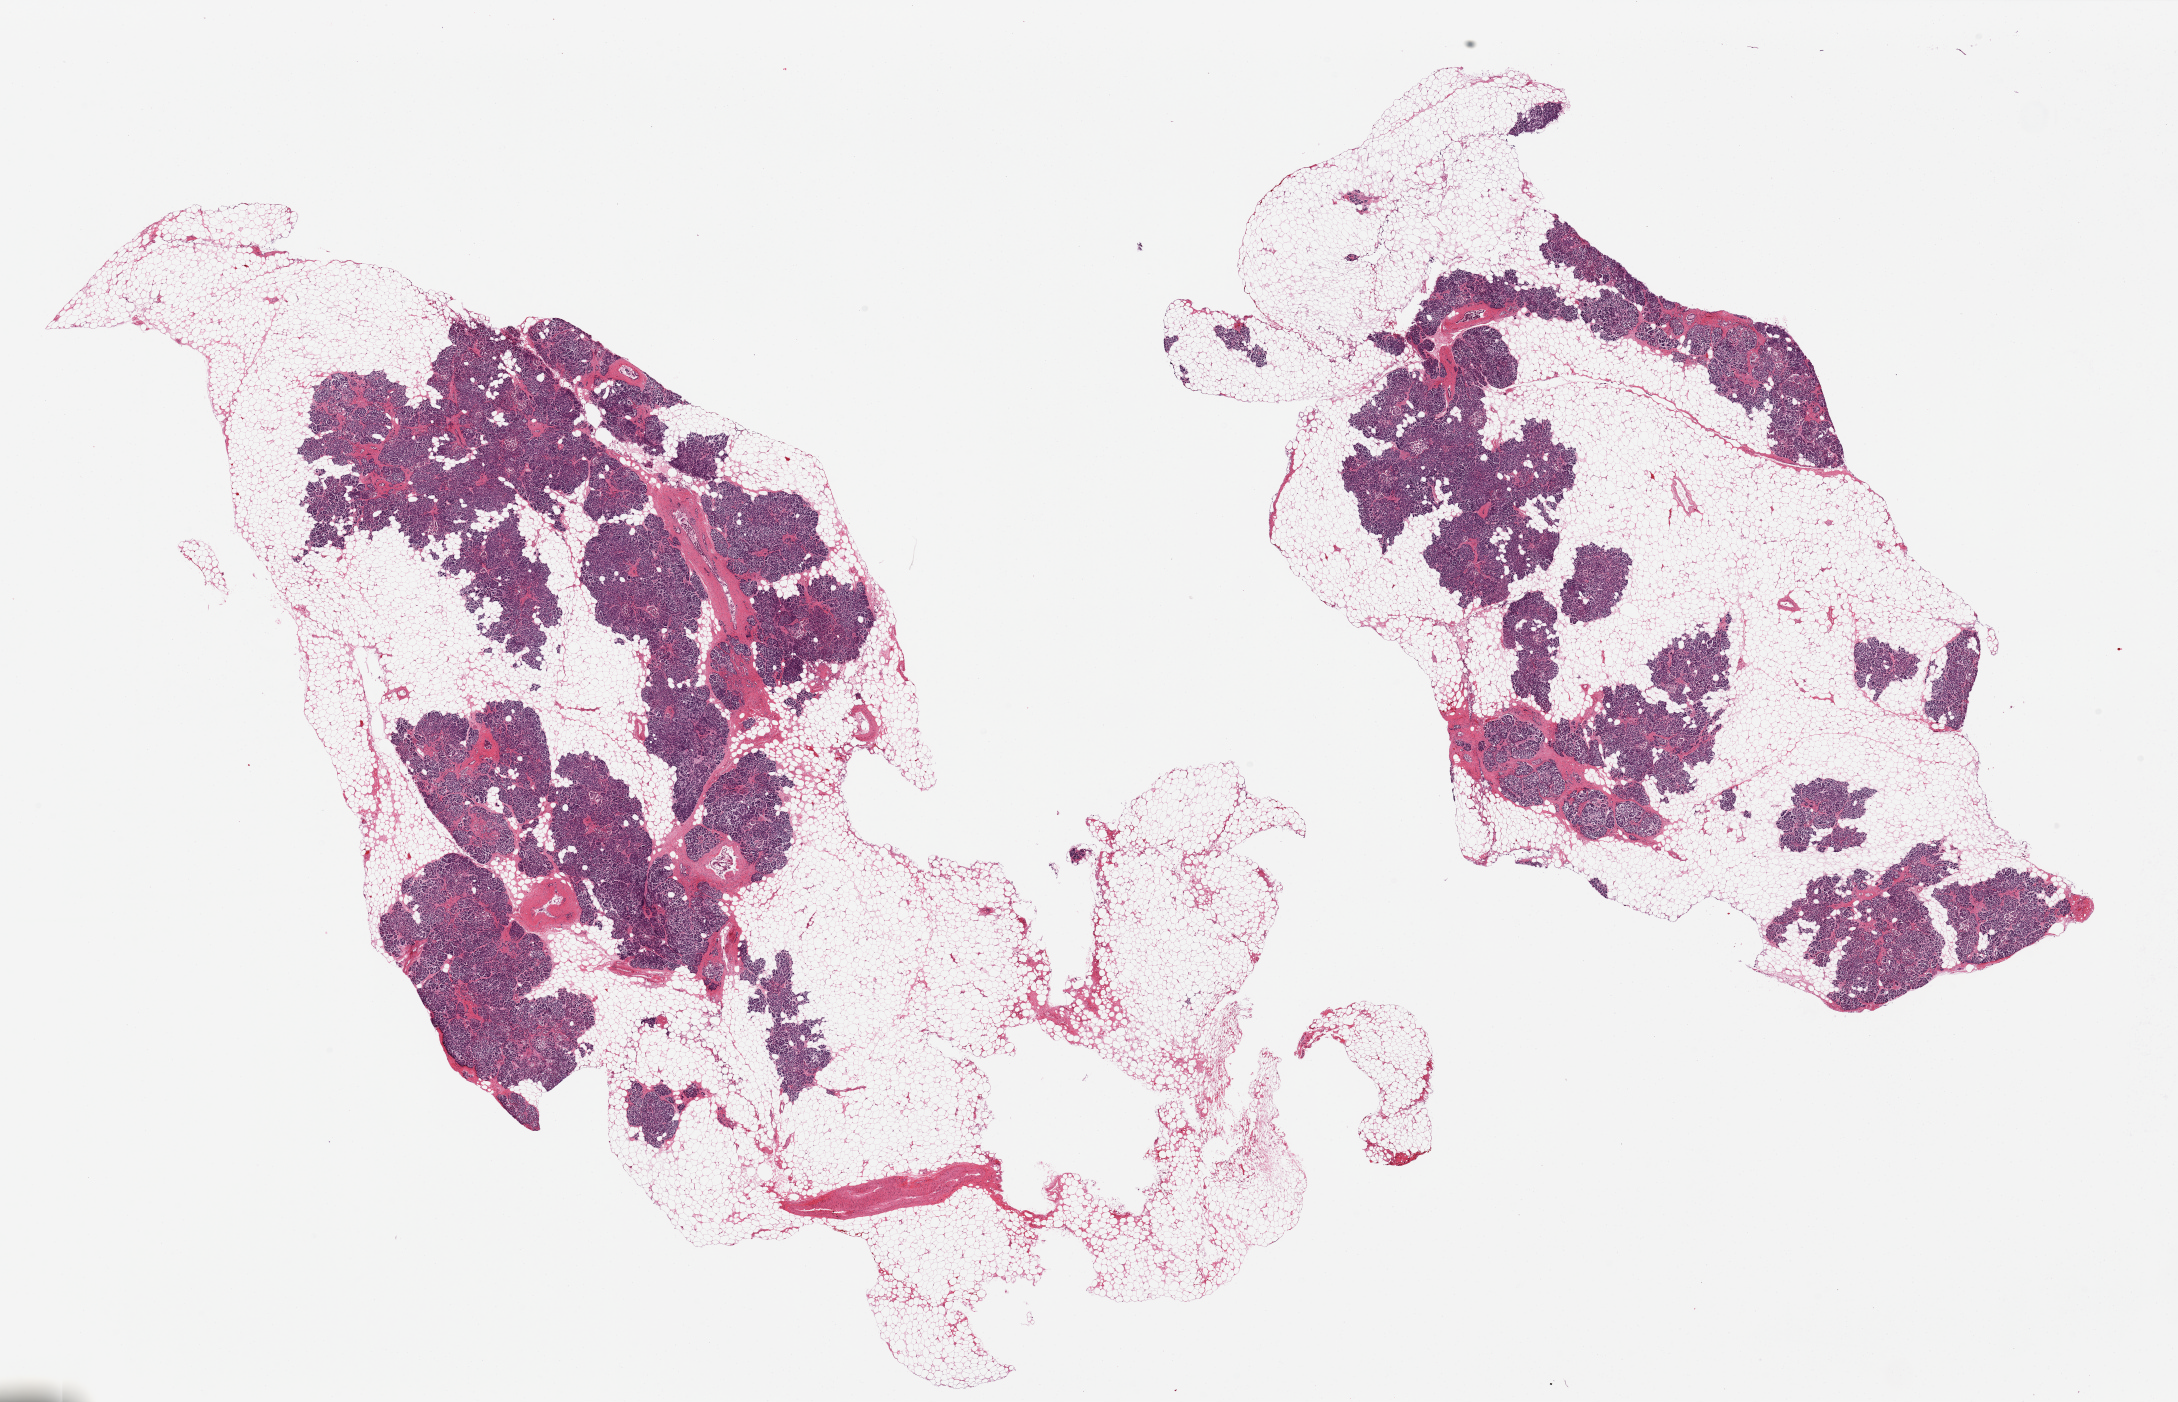
Whole-slide image, hematoxylin and eosin (H&E) stain, brightfield — shown as a low-resolution overview of the whole scanned area (about 34.5 x 22.2 mm); PAXgene-fixed paraffin-embedded (PFPE) section; section of pancreas (target tissue); donor tissue sample. Donor: male.
Pathologist's review note for this sample: 2 pieces, up to 70% fat (attached and internal), some fibrosis and atrophy.